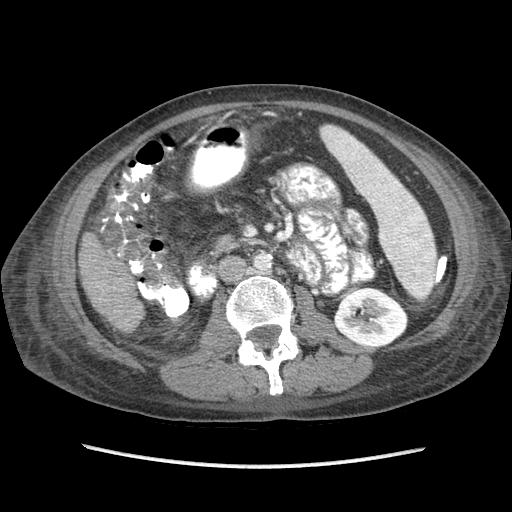
Contrast-enhanced abdominal CT (liver protocol), one axial slice. Position 21 of 87 along the scan axis. Reconstruction kernel STANDARD. Soft-tissue window (W 400 / L 40 HU). 2.5 mm slice thickness. 512 × 512 image matrix, field of view 340 × 340 mm. From the clinical record (not read from this slice): diagnosis: hepatocellular carcinoma (patient treated with transarterial chemoembolisation; whether this scan precedes or follows treatment is not stated here); TNM stage (as recorded): Stage-IIIB; Child-Pugh class: A.
Outlined on this slice (semi-automatically segmented with operator editing):
- liver parenchyma outside the tumour (the mass and vessels are separate outlines, so this box may not span the whole liver): bounding box [x1, y1, x2, y2] px = [78, 232, 144, 330]